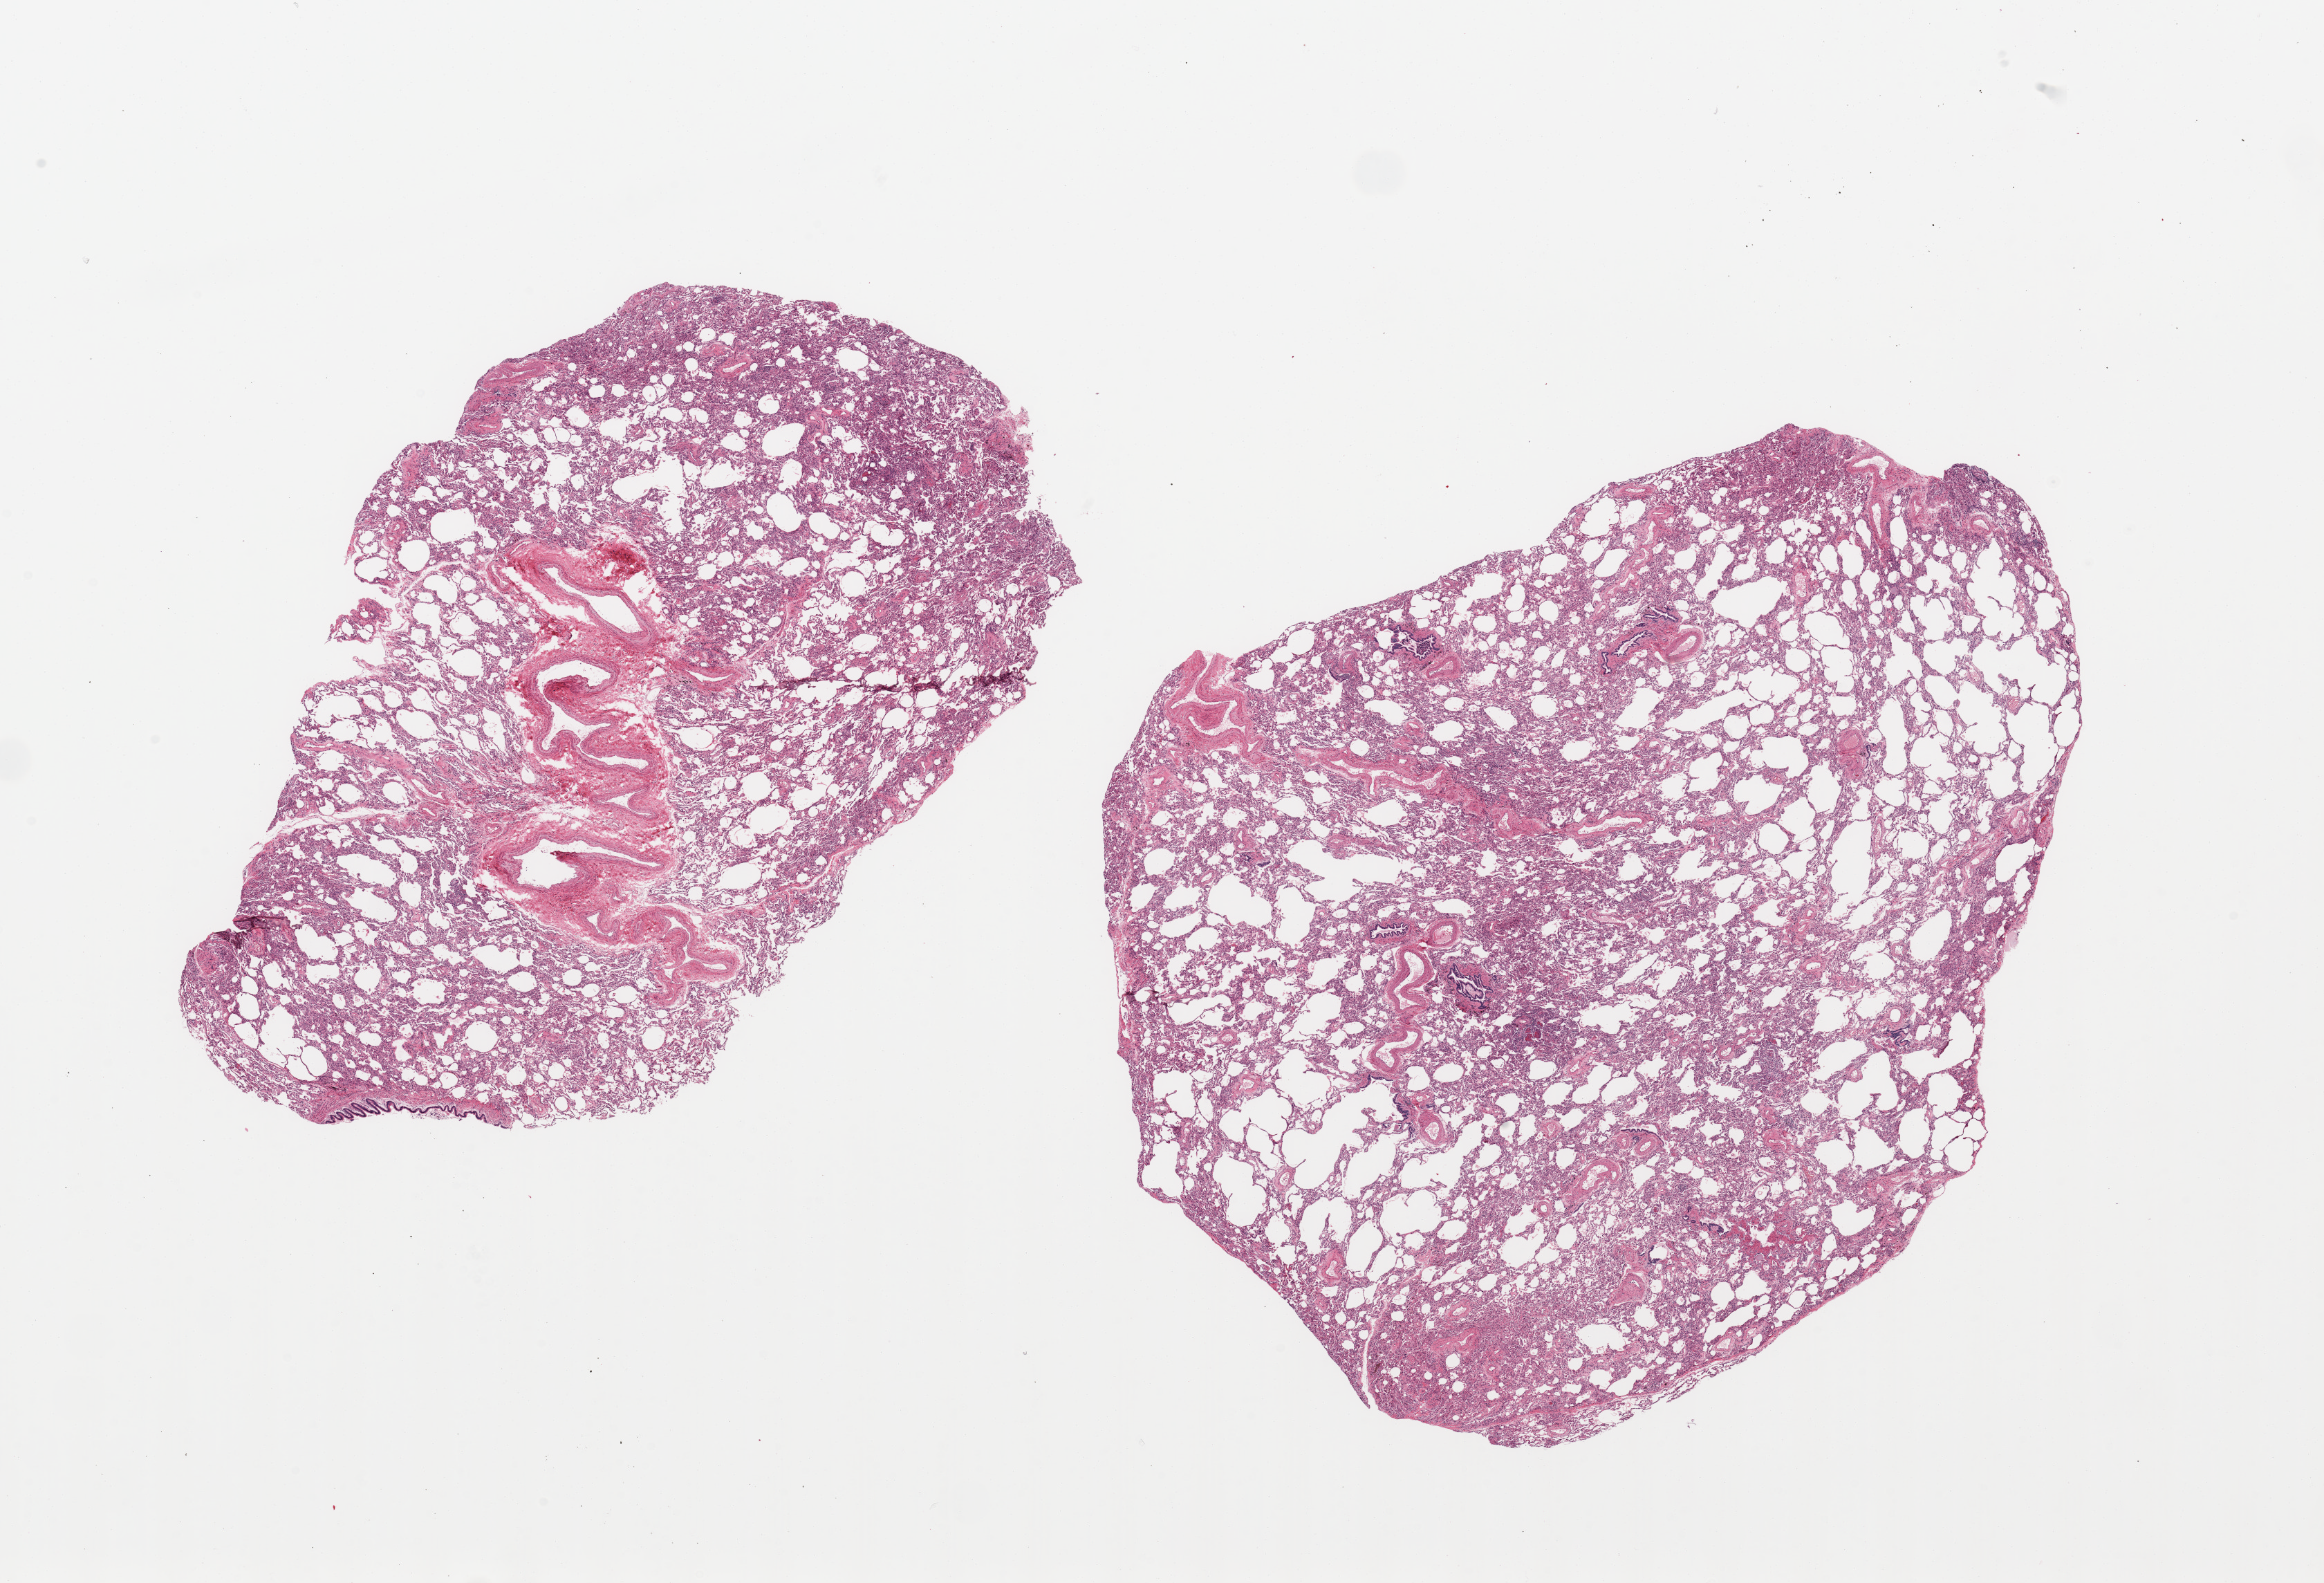
Haematoxylin and eosin whole-slide image, brightfield, low-resolution overview of the scanned area, about 26.6 x 18.1 mm; PAXgene-fixed paraffin-embedded (PFPE) section; target tissue: lung; tissue donor sample. Donor sex: male.
Reviewer comment on this tissue sample: 2 pieces; no lesions.